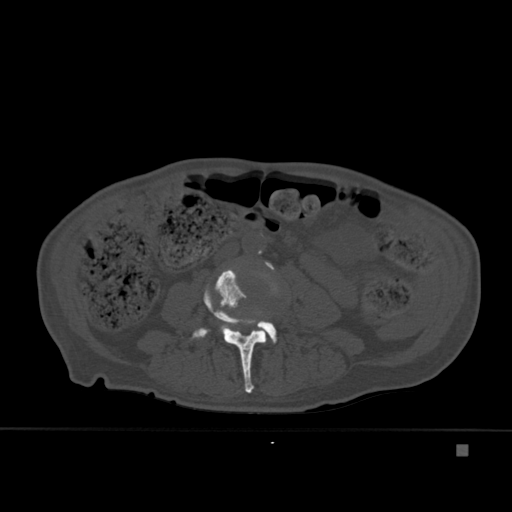
CT including the spine, one axial slice; bone window (W 1800 / L 400 HU); 512 × 512 image matrix. Patient: male, 75 years. Case-level facts recorded for this patient, not image findings: primary cancer: prostate.
Outlined on this slice (semi-automatically segmented with operator editing):
- L3 vertebra: bounding box (x1, y1, x2, y2) in pixels: (191, 268, 267, 394)
- L4 vertebra: (220, 262, 277, 344)